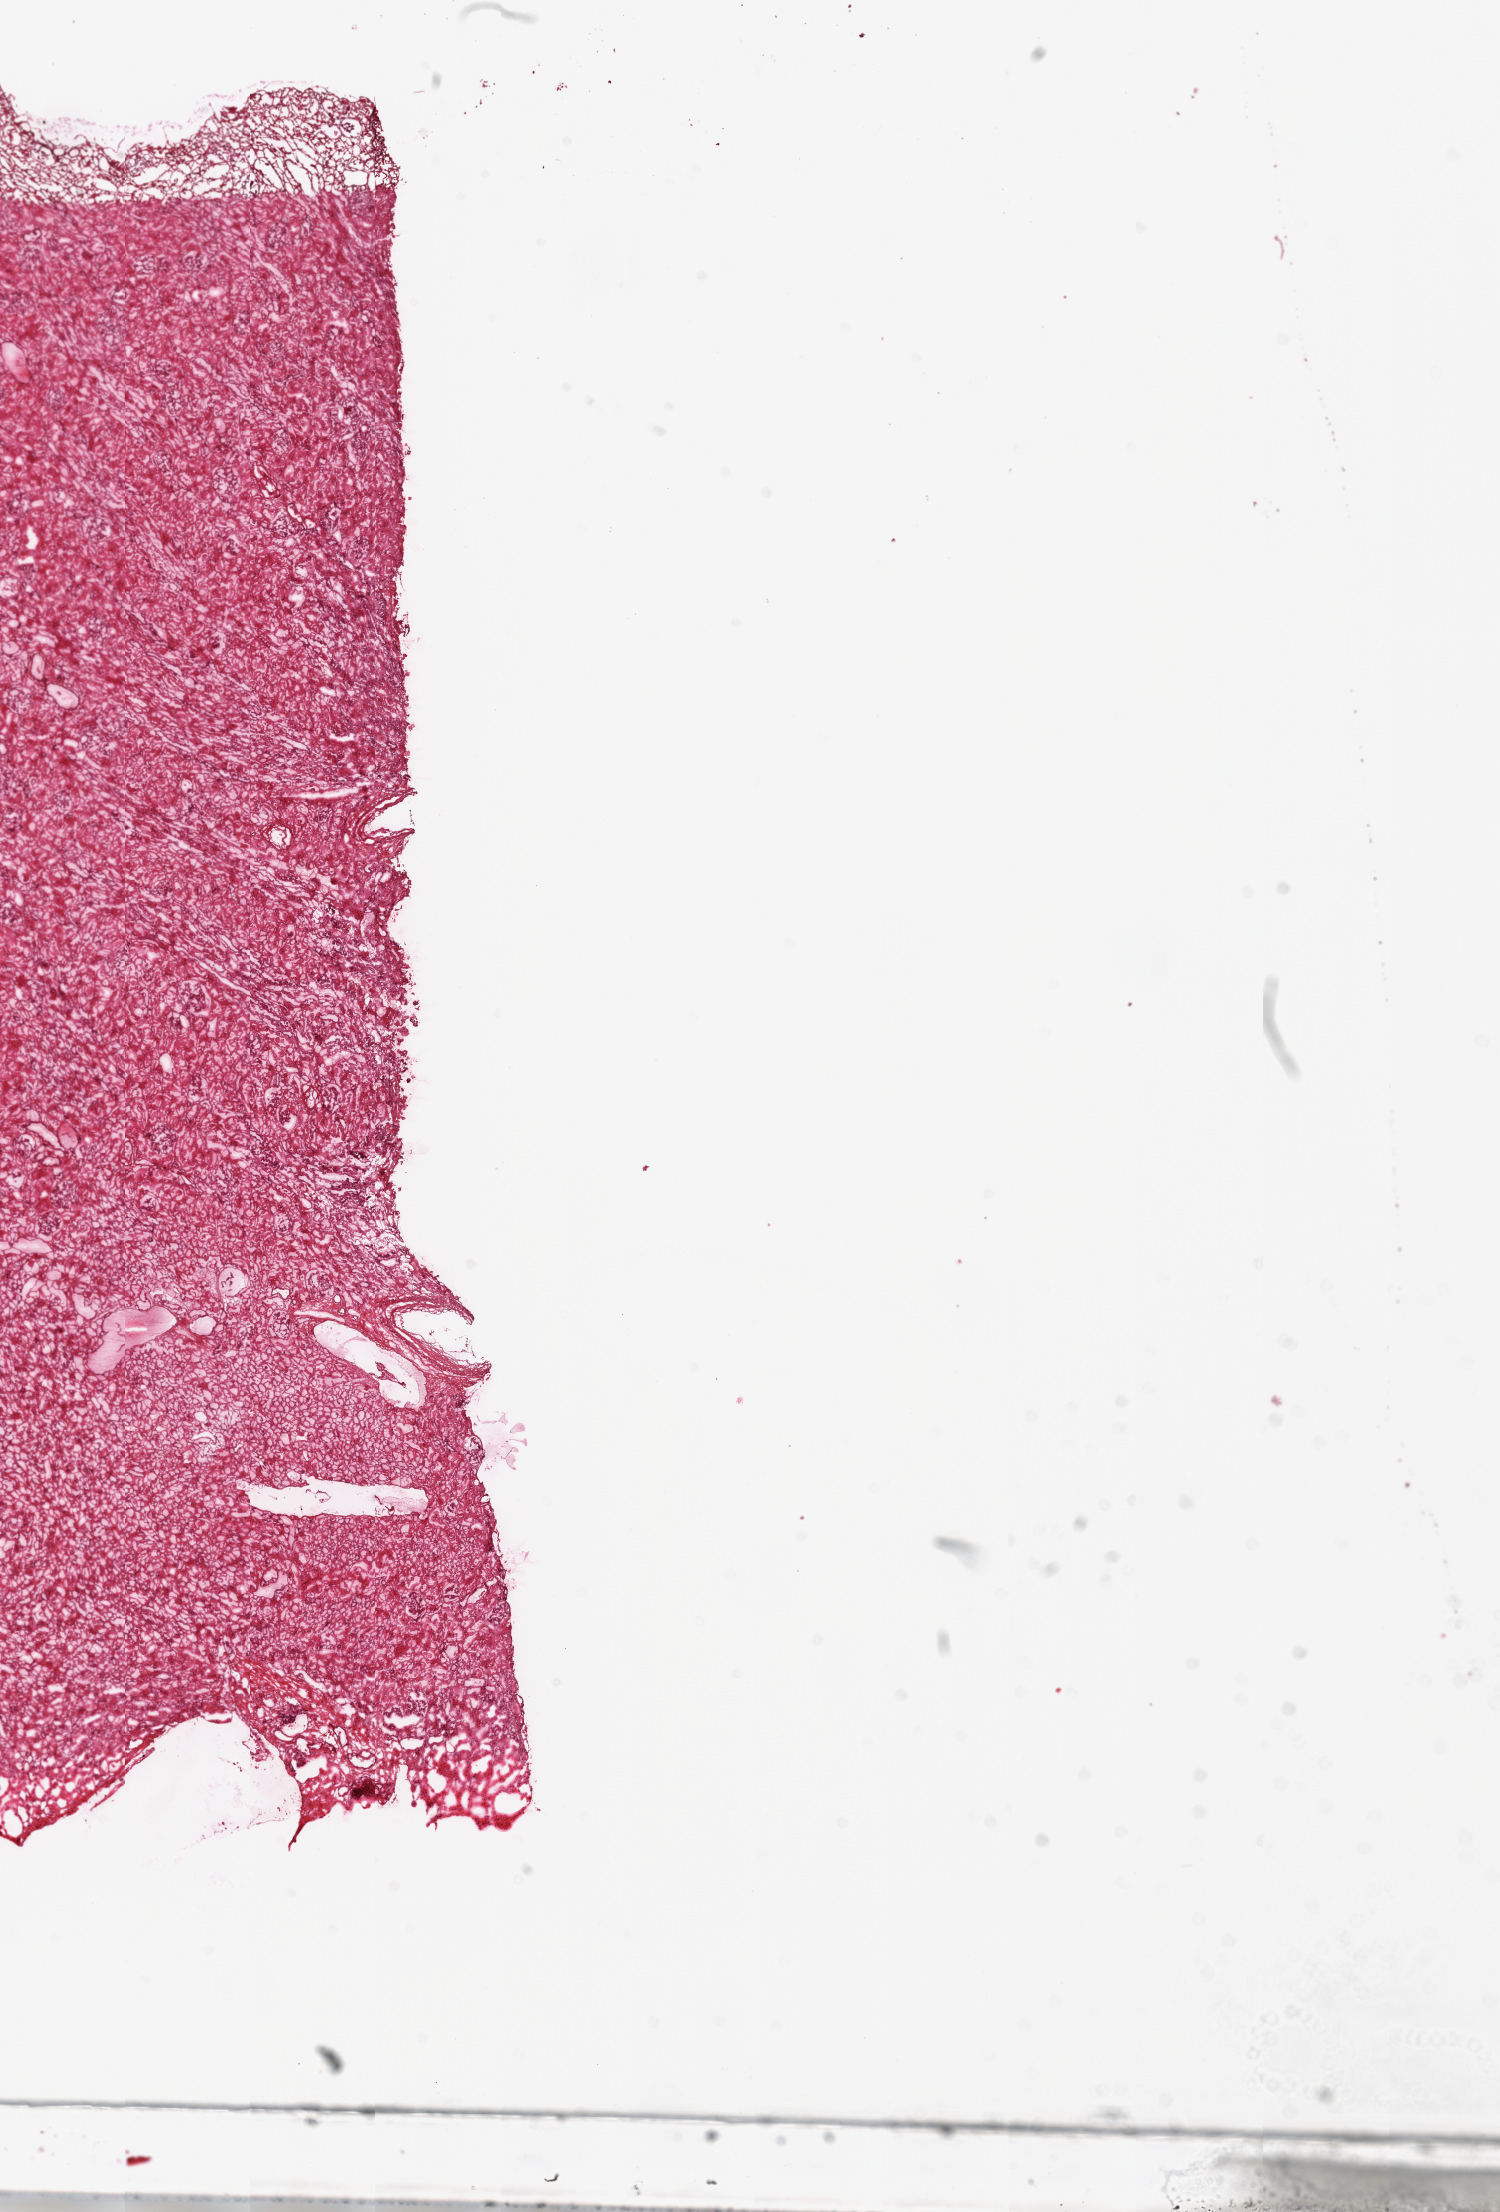
Digitized Hematoxylin and eosin (H&E) stained tissue section (whole slide) — low-resolution overview of the scanned area, about 12.0 x 17.7 mm. Frozen section. Solid tissue normal (non-tumour tissue) sample from the kidney. Patient: female, age at initial diagnosis 54 years.
• this section: solid tissue normal (non-tumour) sample from the same patient
• patient diagnosis: Clear cell adenocarcinoma, NOS